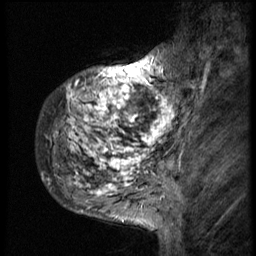
Breast MRI (dynamic contrast-enhanced), one sagittal slice. Position 12 of 58 along the scan axis. 3 images stored at this slice position (order not interpretable as contrast timing). 1.5 T. TE 4.2 ms, TR 9 ms. 2.5 mm slice thickness. 256 × 256 image matrix, field of view 180 × 180 mm. Patient: female, 50 years. Case-level facts recorded for this patient, not image findings: setting: breast cancer imaged before/during neoadjuvant chemotherapy; receptor status: triple-negative.
Annotated regions visible in this slice (semi-automatically segmented with operator editing):
- analysis volume of interest (the breast-tissue region the enhancement analysis was run in; not a lesion): bounding box <37,48,186,214> (left, top, right, bottom; pixels)
- tumour enhancement mask (voxels above the 140 % enhancement threshold inside the analysis volume of interest): <50,56,182,212>